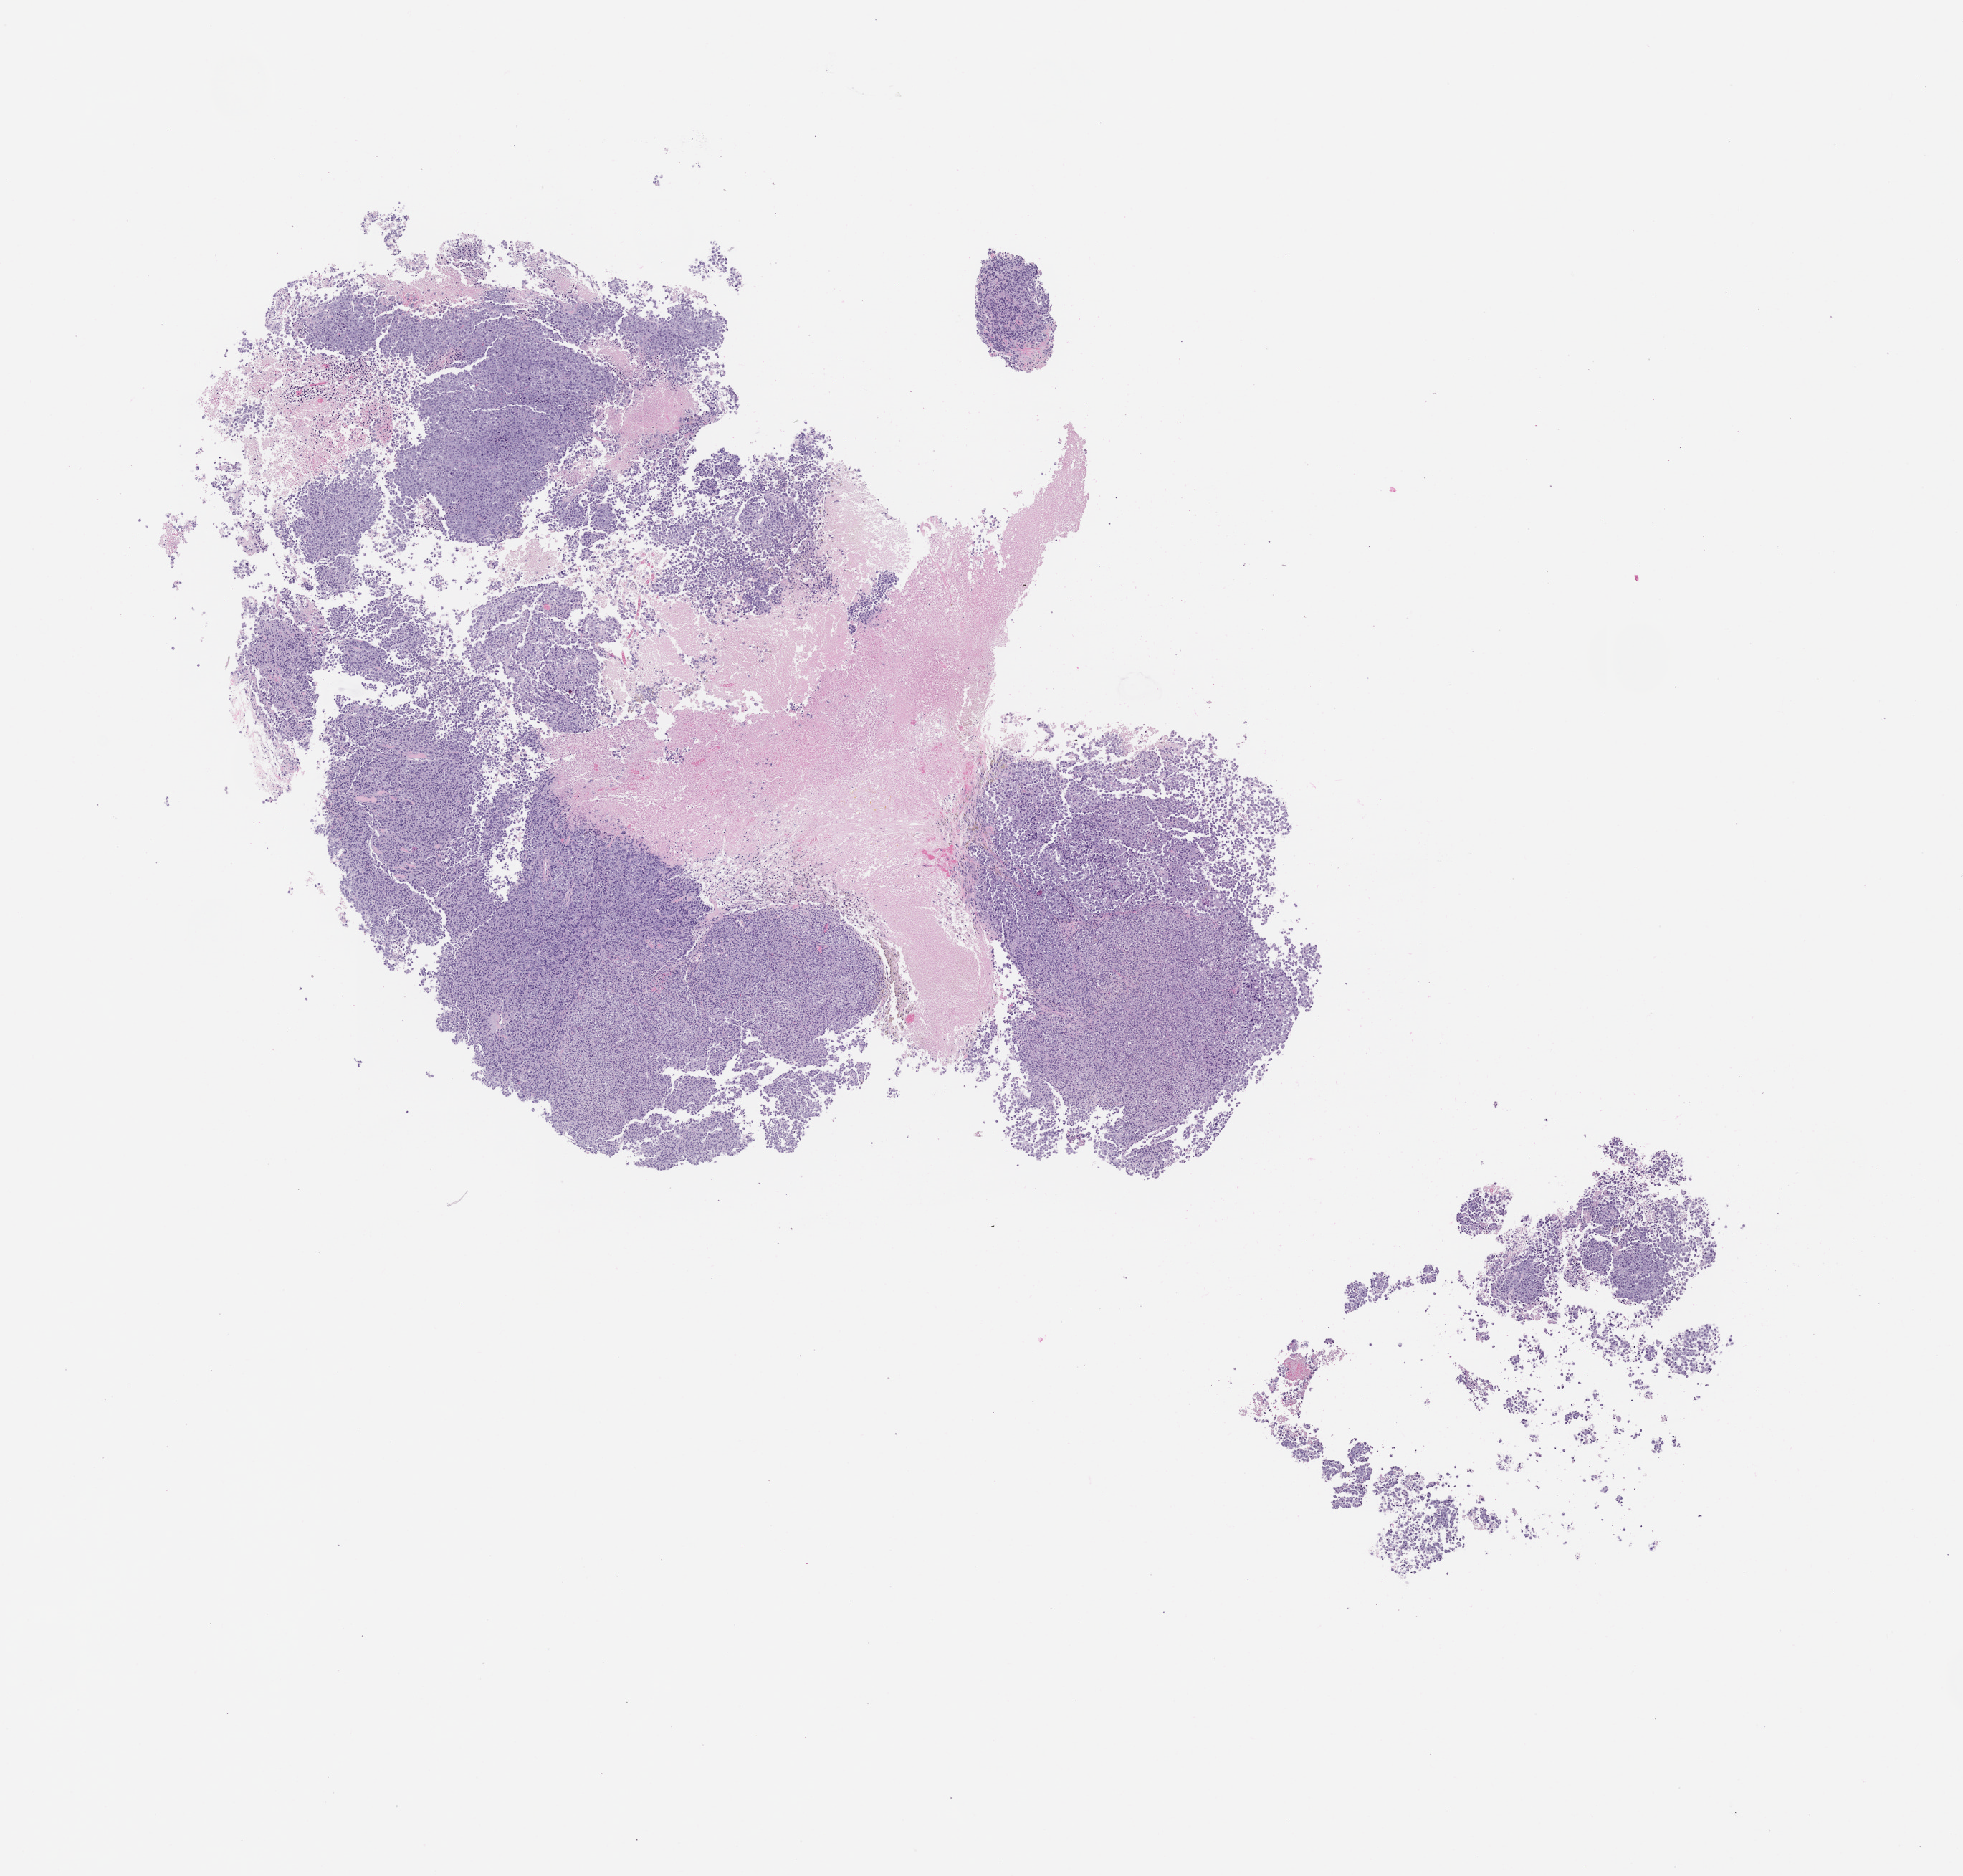
Hematoxylin and eosin (H&E) whole-slide image of a patient-derived xenograft (PDX) tumor grown in a mouse, passage 3 — a low-resolution overview of the entire scanned area, about 11.0 x 10.5 mm; FFPE section; originating tumor site category: skin.
Originating patient diagnosis: Melanoma.